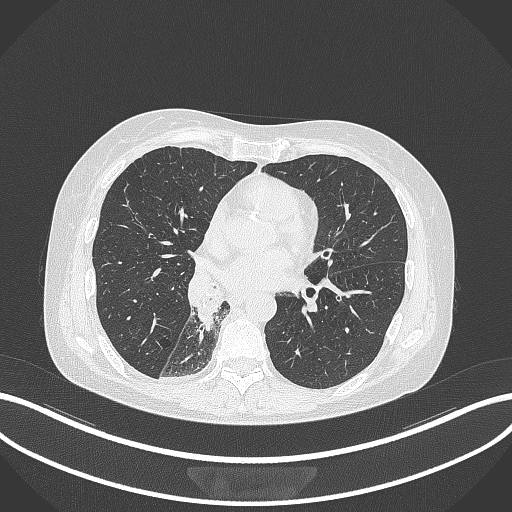
Chest CT, one axial slice. Slice 142 of 329 in the series (ordered by position). Reconstruction kernel B70f. Lung window (W 1500 / L -600 HU). 1 mm slice thickness. 512 × 512 image matrix, field of view 400 × 400 mm. Female patient, age 63 years. Case-level facts recorded for this patient, not image findings: clinical TNM (as recorded): T1c N0 M0.
Structures marked on this image (bounding box drawn by a radiologist):
- lung tumour (recorded histology: adenocarcinoma): bounding box <195,278,224,334> (left, top, right, bottom; pixels)